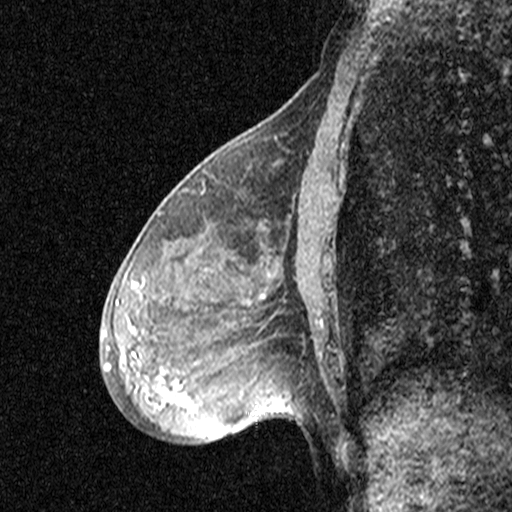
Breast MRI (dynamic contrast-enhanced), one sagittal slice; position 19 of 44 along the scan axis; dynamic contrast-enhanced study with each time point stored as its own series, time point 2 of 3 at this slice position (early post-contrast, ordered by acquisition time); 1.5 T; TE 4.5 ms, TR 11 ms; 3 mm slice thickness; 512 × 512 image matrix, field of view 200 × 200 mm. Female patient, age 53 years. From the clinical record (not read from this slice): setting: breast cancer imaged before/during neoadjuvant chemotherapy; receptor status: HR-positive, HER2-negative.
Structures marked on this image (semi-automatically segmented with operator editing):
- analysis volume of interest (the breast-tissue region the enhancement analysis was run in; not a lesion): bounding box <88,176,313,423> (left, top, right, bottom; pixels)
- tumour enhancement mask (voxels above the 90 % enhancement threshold inside the analysis volume of interest): <134,284,190,404>